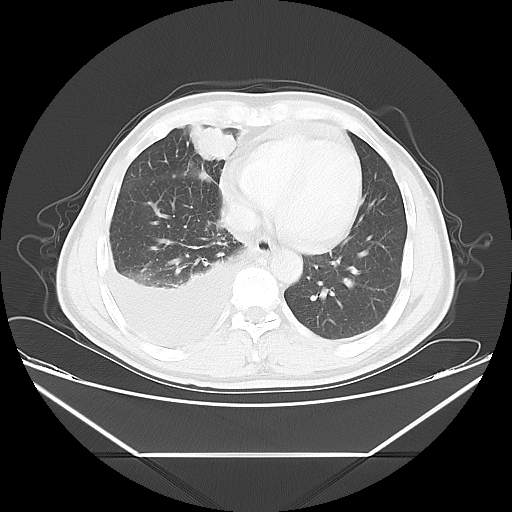
Chest CT, one axial slice. 120 kVp. Lung window (W 1500 / L -600 HU). 5 mm slice thickness. 512 × 512 image matrix. Patient: male, 57 years. Case-level facts recorded for this patient, not image findings: clinical TNM (as recorded): T2 N3 M1.
Outlined on this slice (bounding box drawn by a radiologist):
- lung tumour (recorded histology: adenocarcinoma): bounding box (x1, y1, x2, y2) in pixels: (183, 124, 240, 173)